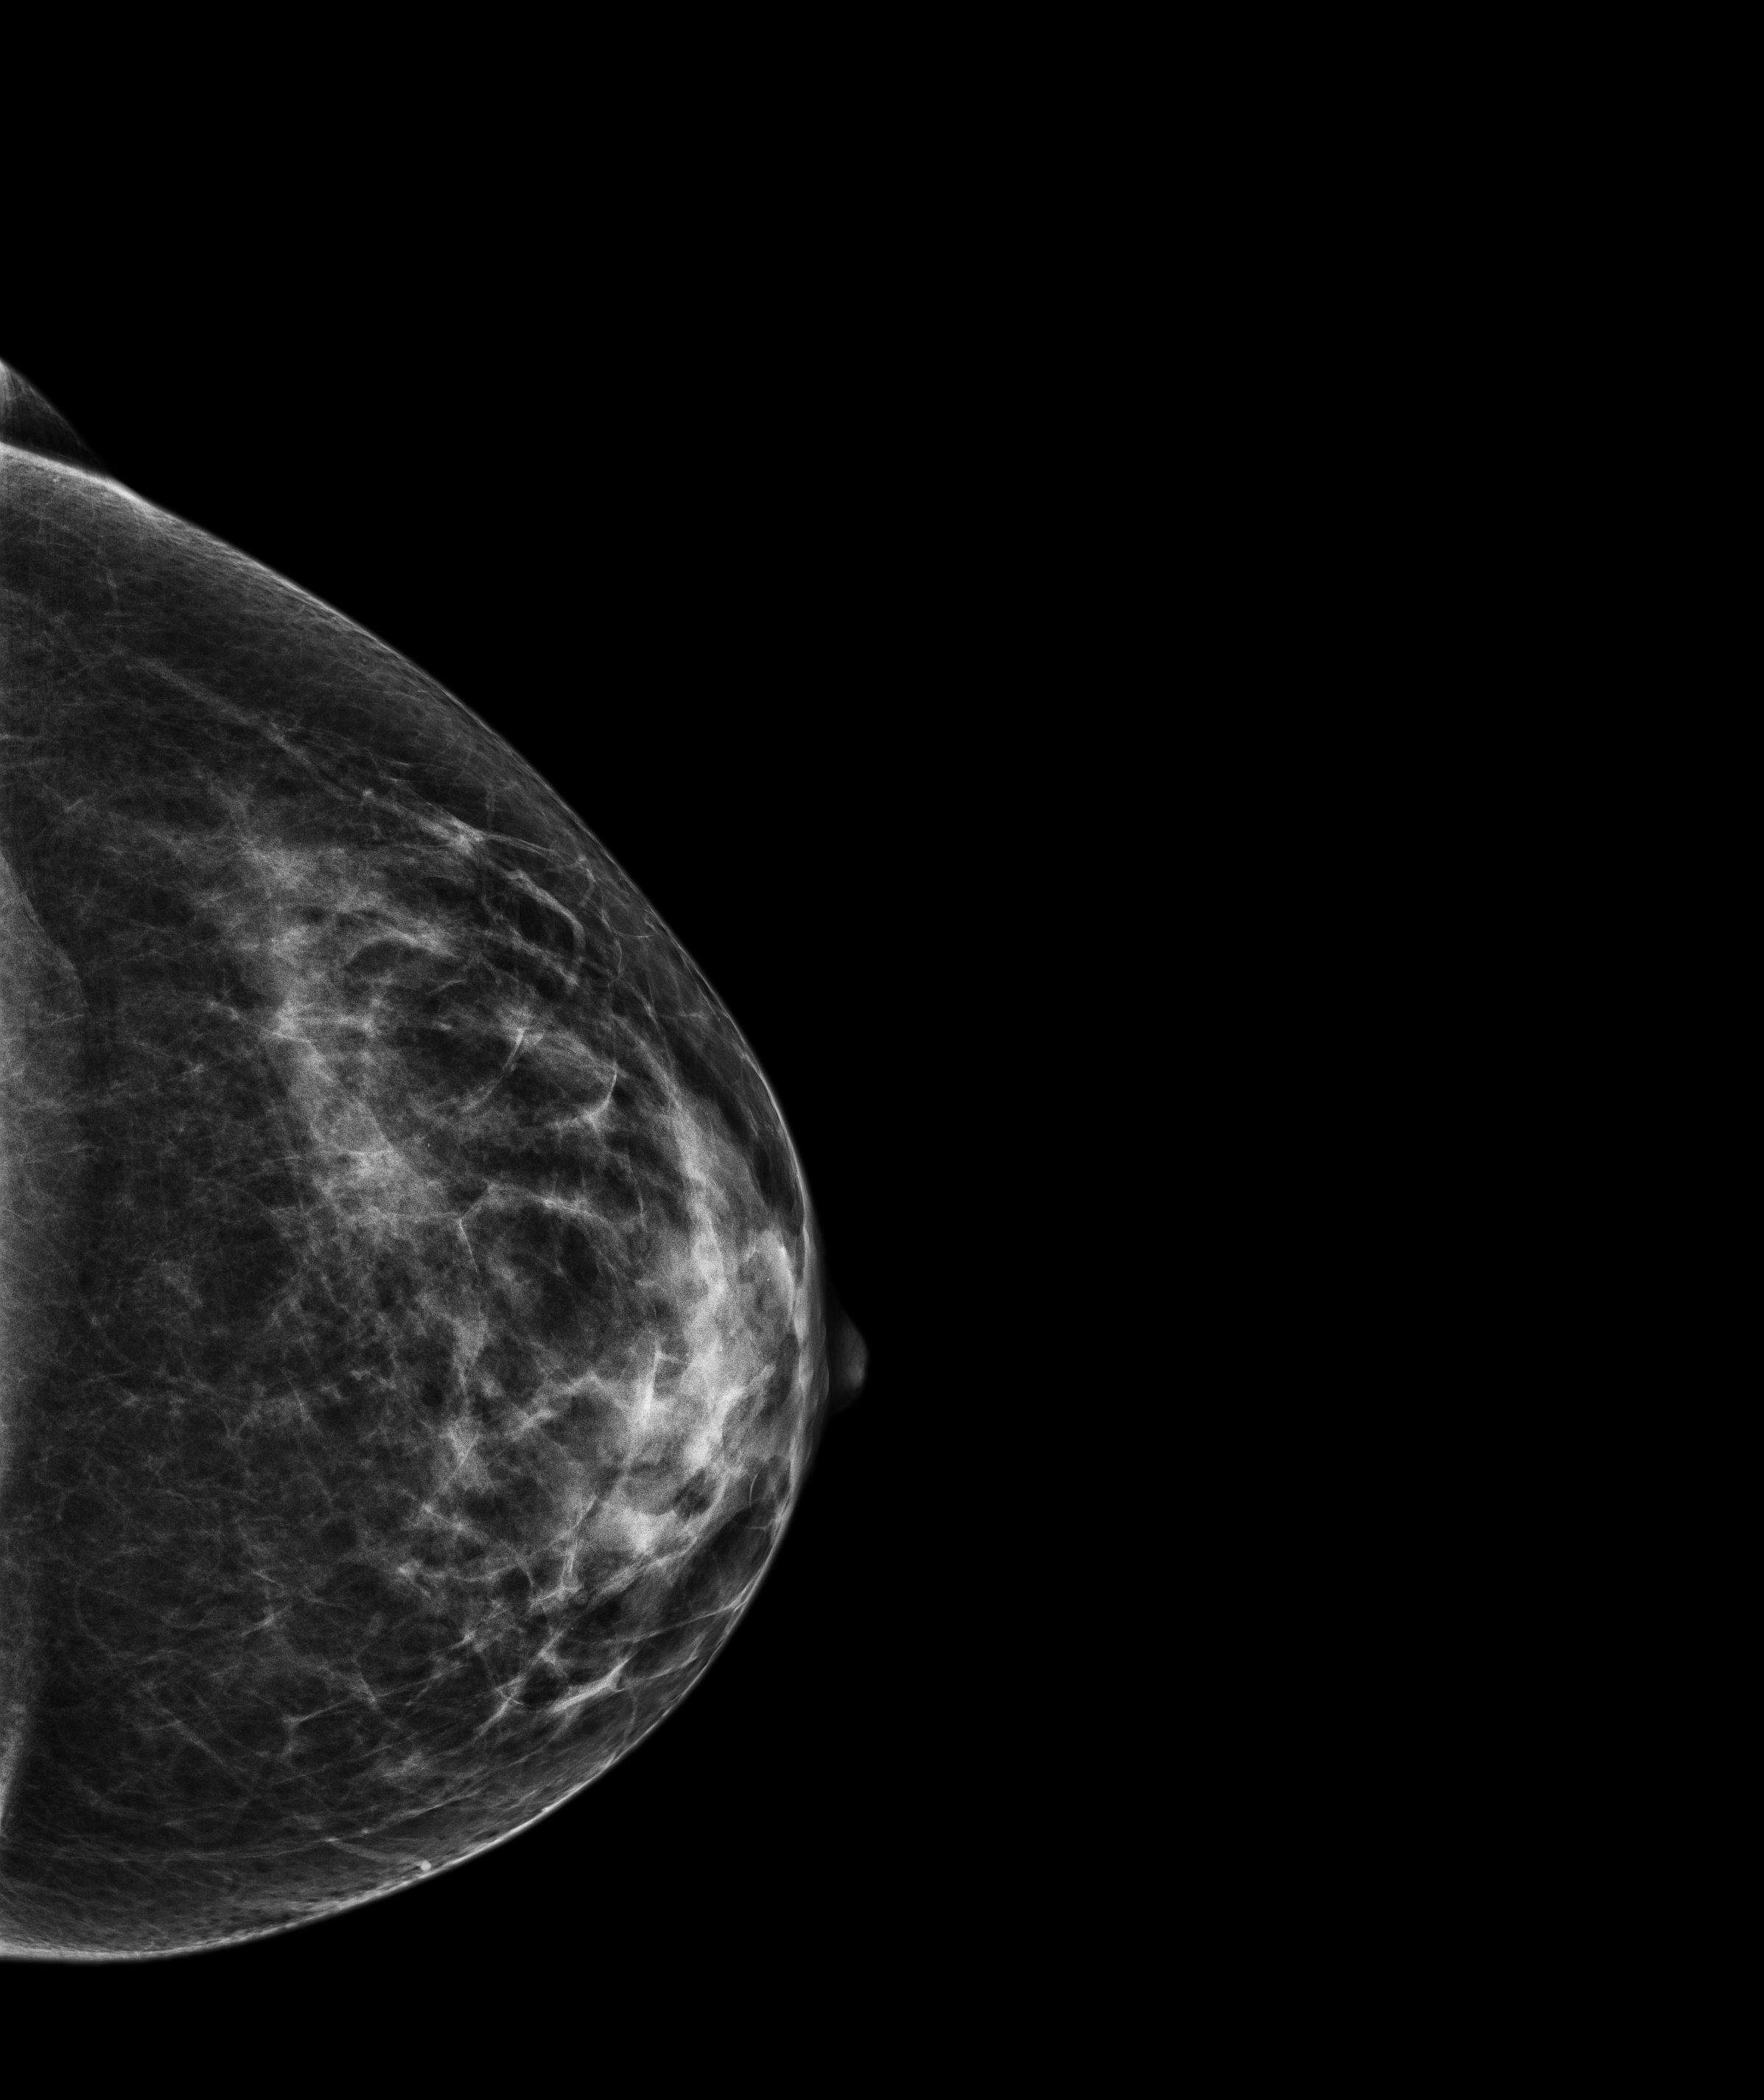
Screening examination; system: Senographe Pristina. Patient: female, 47 years.
Image type: full-field digital mammogram. Breast: left. Projection: cranio-caudal projection.